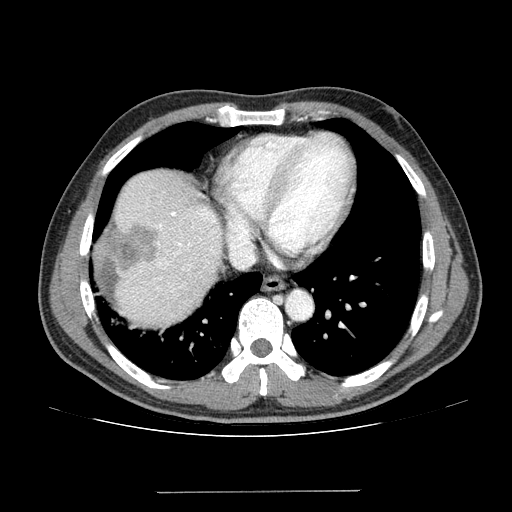
Contrast-enhanced abdominal CT (liver protocol), one axial slice. Slice 119 of 131 in the series (ordered by position). Reconstruction kernel STANDARD. 100 kVp. One of 2 acquisitions stored at this slice position. Soft-tissue window (W 400 / L 40 HU). 2.5 mm slice thickness. 512 × 512 image matrix, field of view 380 × 380 mm. Case-level facts recorded for this patient, not image findings: diagnosis: hepatocellular carcinoma (patient treated with transarterial chemoembolisation; whether this scan precedes or follows treatment is not stated here); TNM stage (as recorded): Stage-I; Child-Pugh class: A; tumour differentiation: poorly differentiated.
Outlined on this slice (semi-automatically segmented with operator editing):
- liver parenchyma outside the tumour (the mass and vessels are separate outlines, so this box may not span the whole liver): bounding box [x1, y1, x2, y2] px = [94, 170, 222, 326]
- mass: [92, 221, 158, 271]
- liver vessels: [141, 209, 216, 301]